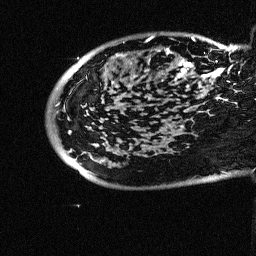
Breast MRI (dynamic contrast-enhanced), one sagittal slice. Slice 12 of 64 in the series (ordered by position). Dynamic contrast-enhanced study with each time point stored as its own series, time point 2 of 3 at this slice position (early post-contrast, ordered by acquisition time). 1.5 T. TE 4.5 ms, TR 11 ms. 256 × 256 image matrix, field of view 200 × 200 mm. Female patient, age 38 years. From the clinical record (not read from this slice): setting: breast cancer imaged before/during neoadjuvant chemotherapy; receptor status: HR-positive, HER2-negative.
Structures marked on this image (semi-automatically segmented with operator editing):
- analysis volume of interest (the breast-tissue region the enhancement analysis was run in; not a lesion): bounding box [x1, y1, x2, y2] px = [88, 21, 252, 126]
- tumour enhancement mask (voxels above the 90 % enhancement threshold inside the analysis volume of interest): [120, 36, 240, 78]